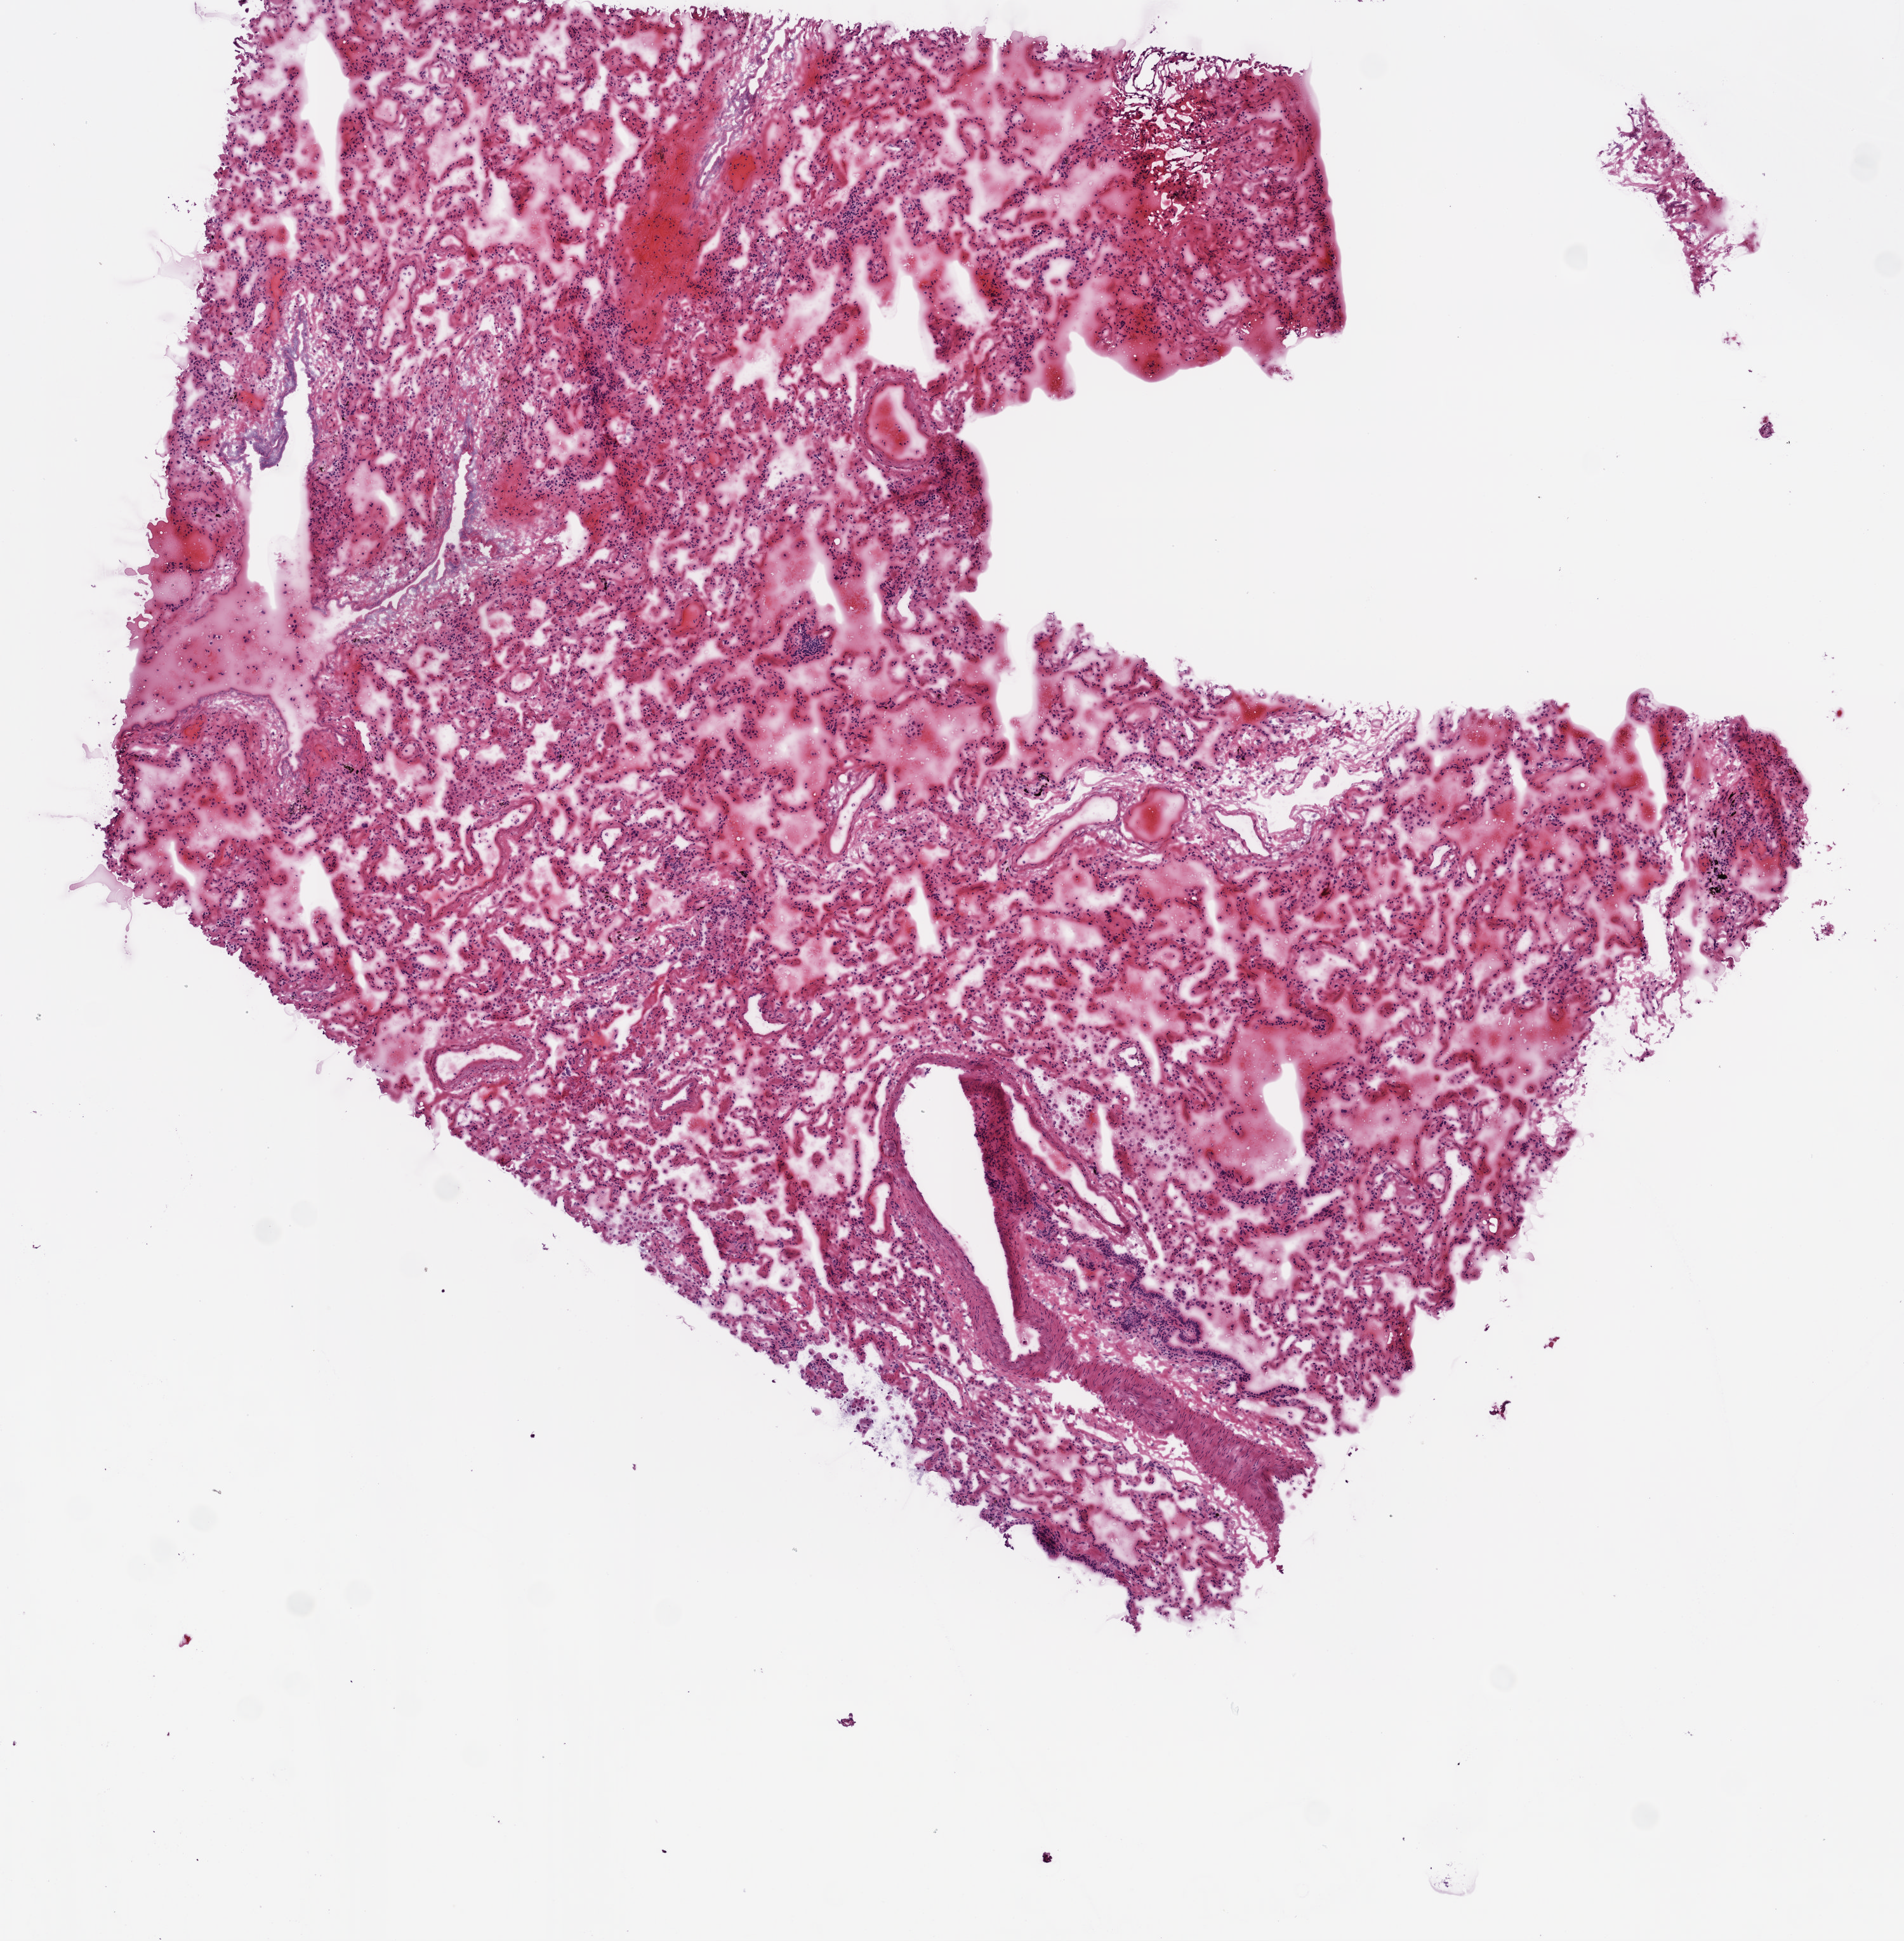
H&E whole-slide image — low-resolution overview of the scanned area, about 6.0 x 6.1 mm (slide scanned at 20x); frozen section; lung, solid tissue normal (non-tumour tissue) sample. Patient: female, age at initial diagnosis 66 years.
This section: solid tissue normal sample (biorepository sample class). Patient diagnosis: Invasive micropapillary carcinoma (upper lobe, lung).